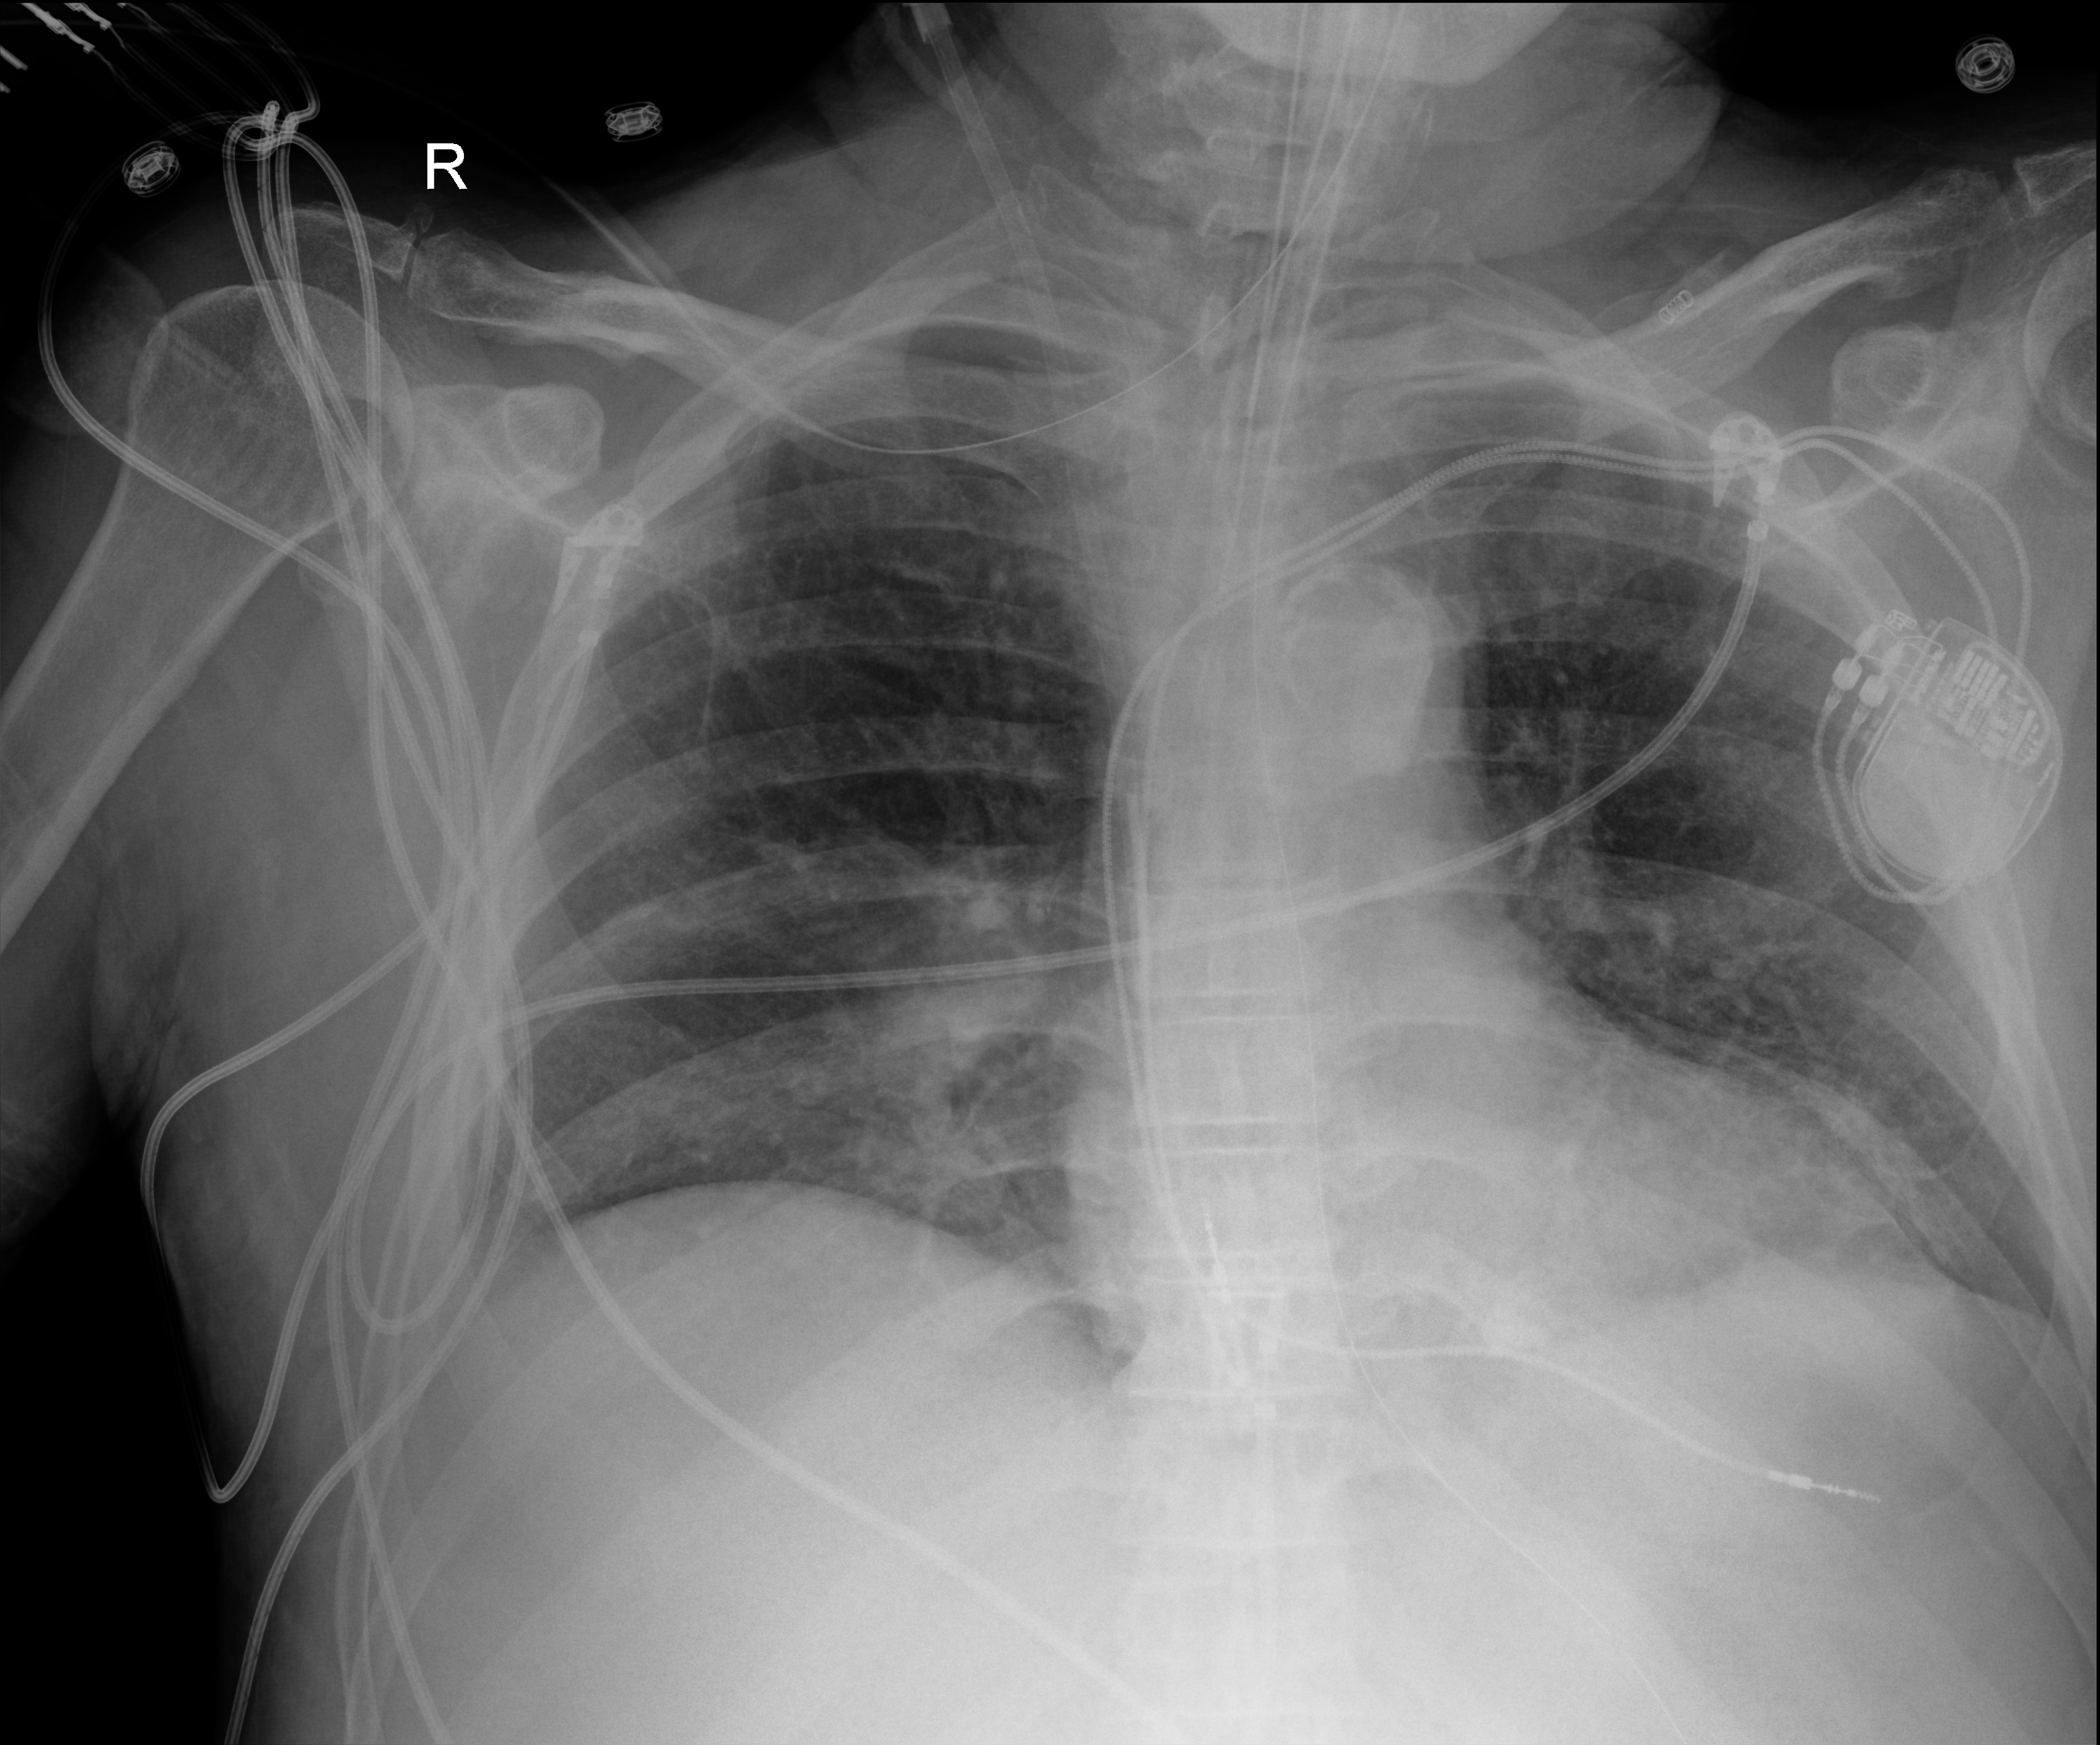
Chest X-ray (portable); anteroposterior (AP) projection. Male patient hospitalised with COVID-19, age 60–74 years.
Hospital-stay facts (about this admission, not read from this image; timing relative to this image not recorded): admitted to intensive care during this hospital stay: yes.